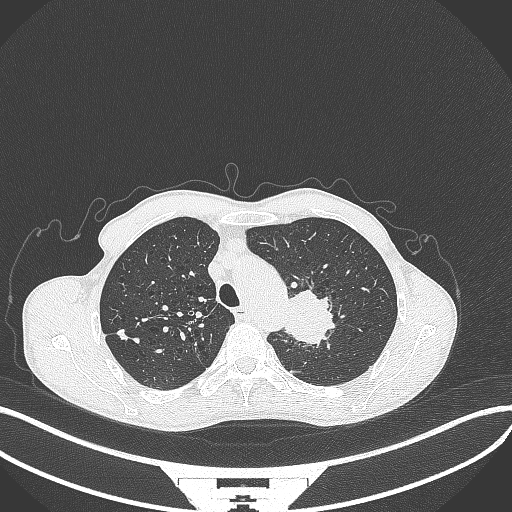
Chest CT, one axial slice. Position 325 of 386 along the scan axis. Lung window (W 1500 / L -600 HU). 512 × 512 image matrix, field of view 400 × 400 mm. Patient: male, 65 years. From the clinical record (not read from this slice): clinical TNM (as recorded): T2b N0 M0.
Structures marked on this image (rectangle marked by the reading radiologist):
- lung tumour (recorded histology: adenocarcinoma): bounding box <281,282,340,349> (left, top, right, bottom; pixels)